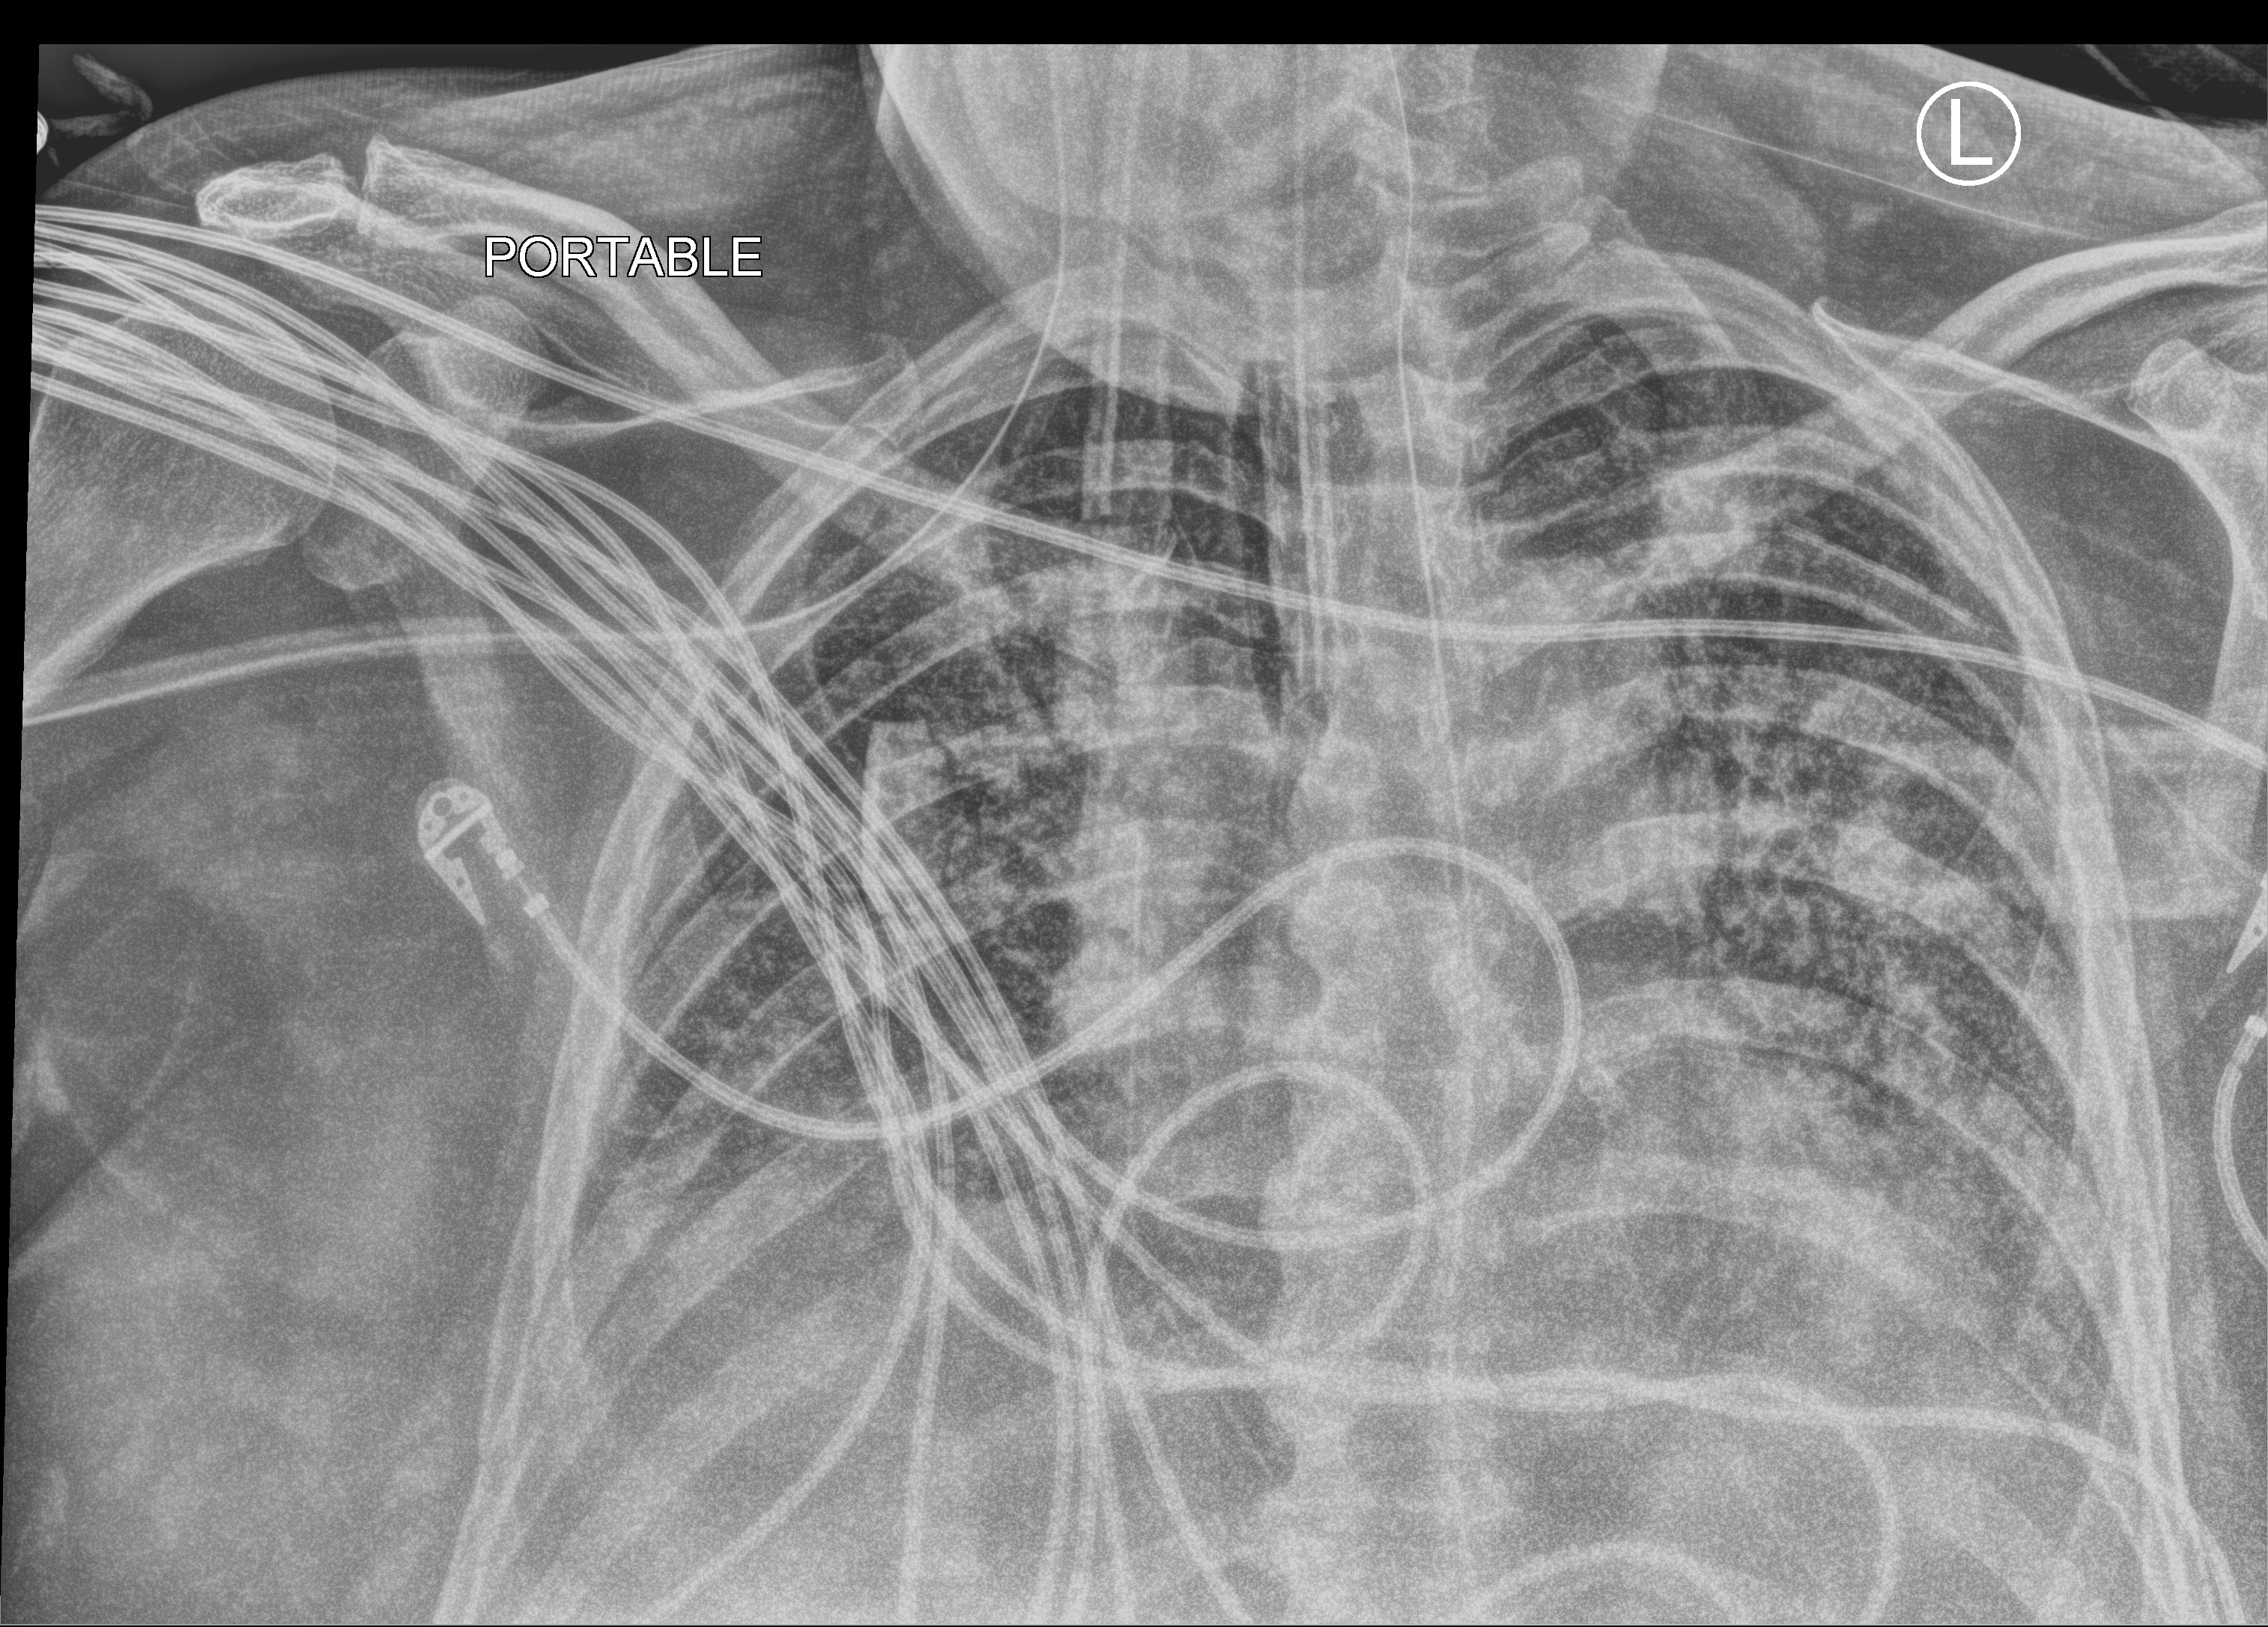
Portable chest radiograph, anteroposterior (AP) projection. Male patient hospitalised with COVID-19, age 60–74 years.
From the hospital-stay record, not from the radiograph (when in the stay this image was taken is not recorded): admitted to intensive care during this hospital stay: yes; mechanically ventilated during this hospital stay: yes; length of hospital stay: 40 days.